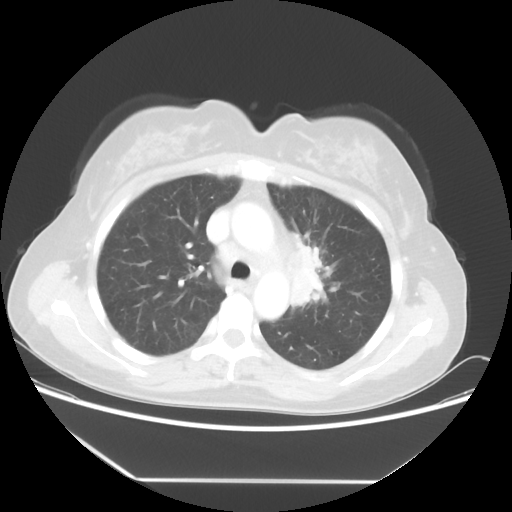
Chest CT, one axial slice. Position 36 of 52 along the scan axis. Lung window (W 1500 / L -600 HU). 5 mm slice thickness. 512 × 512 image matrix, field of view 390 × 390 mm. Female patient, age 50 years. Case-level facts recorded for this patient, not image findings: clinical TNM (as recorded): T2 N3 M0.
Outlined on this slice (rectangle marked by the reading radiologist):
- lung tumour (recorded histology: adenocarcinoma): box from (x=276, y=218) to (x=353, y=332) px